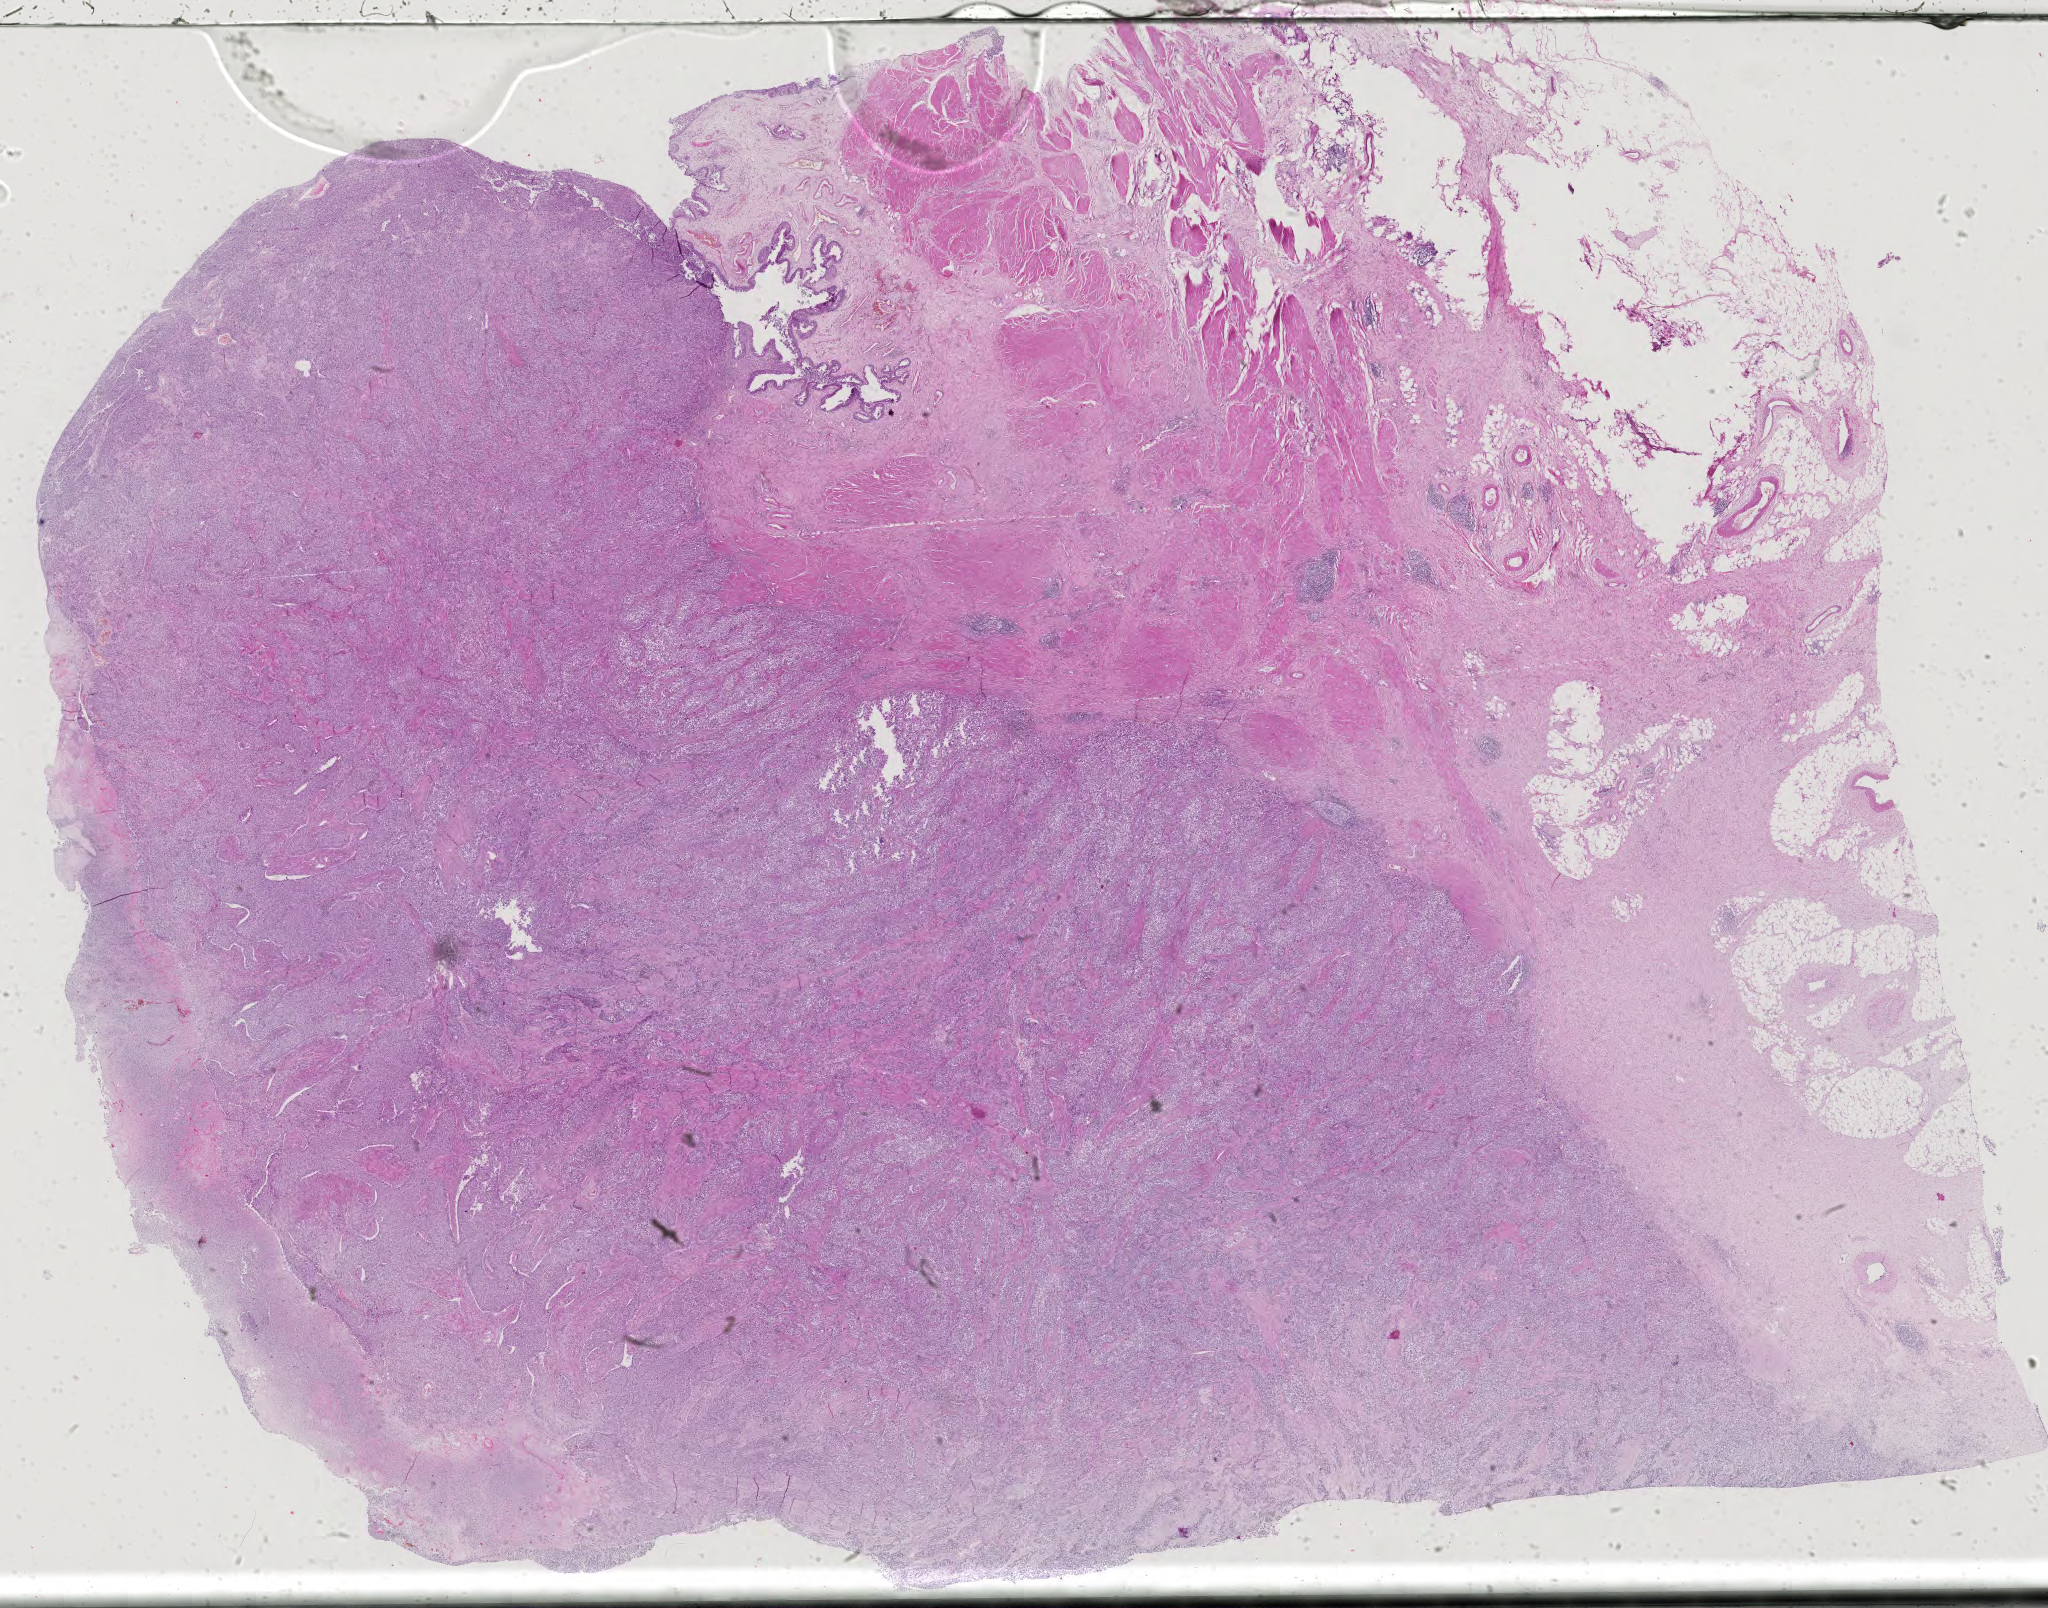
Digitized Hematoxylin and eosin (H&E) stained tissue section (whole slide) — low-resolution overview of the scanned area, about 29.8 x 23.4 mm (acquisition: 40x scan), formalin-fixed paraffin-embedded (FFPE) diagnostic section, primary tumour sample from the bladder. Male patient. Histologic grade: high grade.
Lymph nodes positive (case pathology): 0 of 20 examined. Histologic diagnosis: Transitional cell carcinoma (posterior wall of bladder). AJCC pathologic stage: II (6th edition).